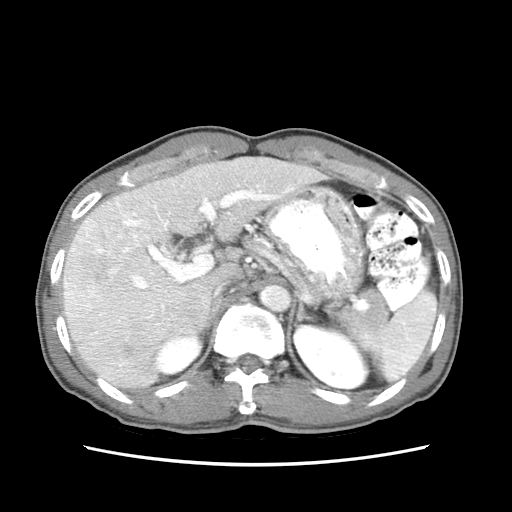
Contrast-enhanced abdominal CT (liver protocol), one axial slice. Position 45 of 79 along the scan axis. 120 kVp. Soft-tissue window (W 400 / L 40 HU). 2.5 mm slice thickness. 512 × 512 image matrix, field of view 320 × 320 mm. Case-level facts recorded for this patient, not image findings: diagnosis: hepatocellular carcinoma (patient treated with transarterial chemoembolisation; whether this scan precedes or follows treatment is not stated here); TNM stage (as recorded): Stage-IIIB; Child-Pugh class: A; tumour differentiation: moderately differentiated.
Outlined on this slice (semi-automatic segmentation, software-assisted and operator-edited):
- liver parenchyma outside the tumour (the mass and vessels are separate outlines, so this box may not span the whole liver): bounding box (x1, y1, x2, y2) in pixels: (62, 156, 324, 390)
- mass: (62, 227, 130, 302)
- liver vessels: (84, 165, 310, 364)